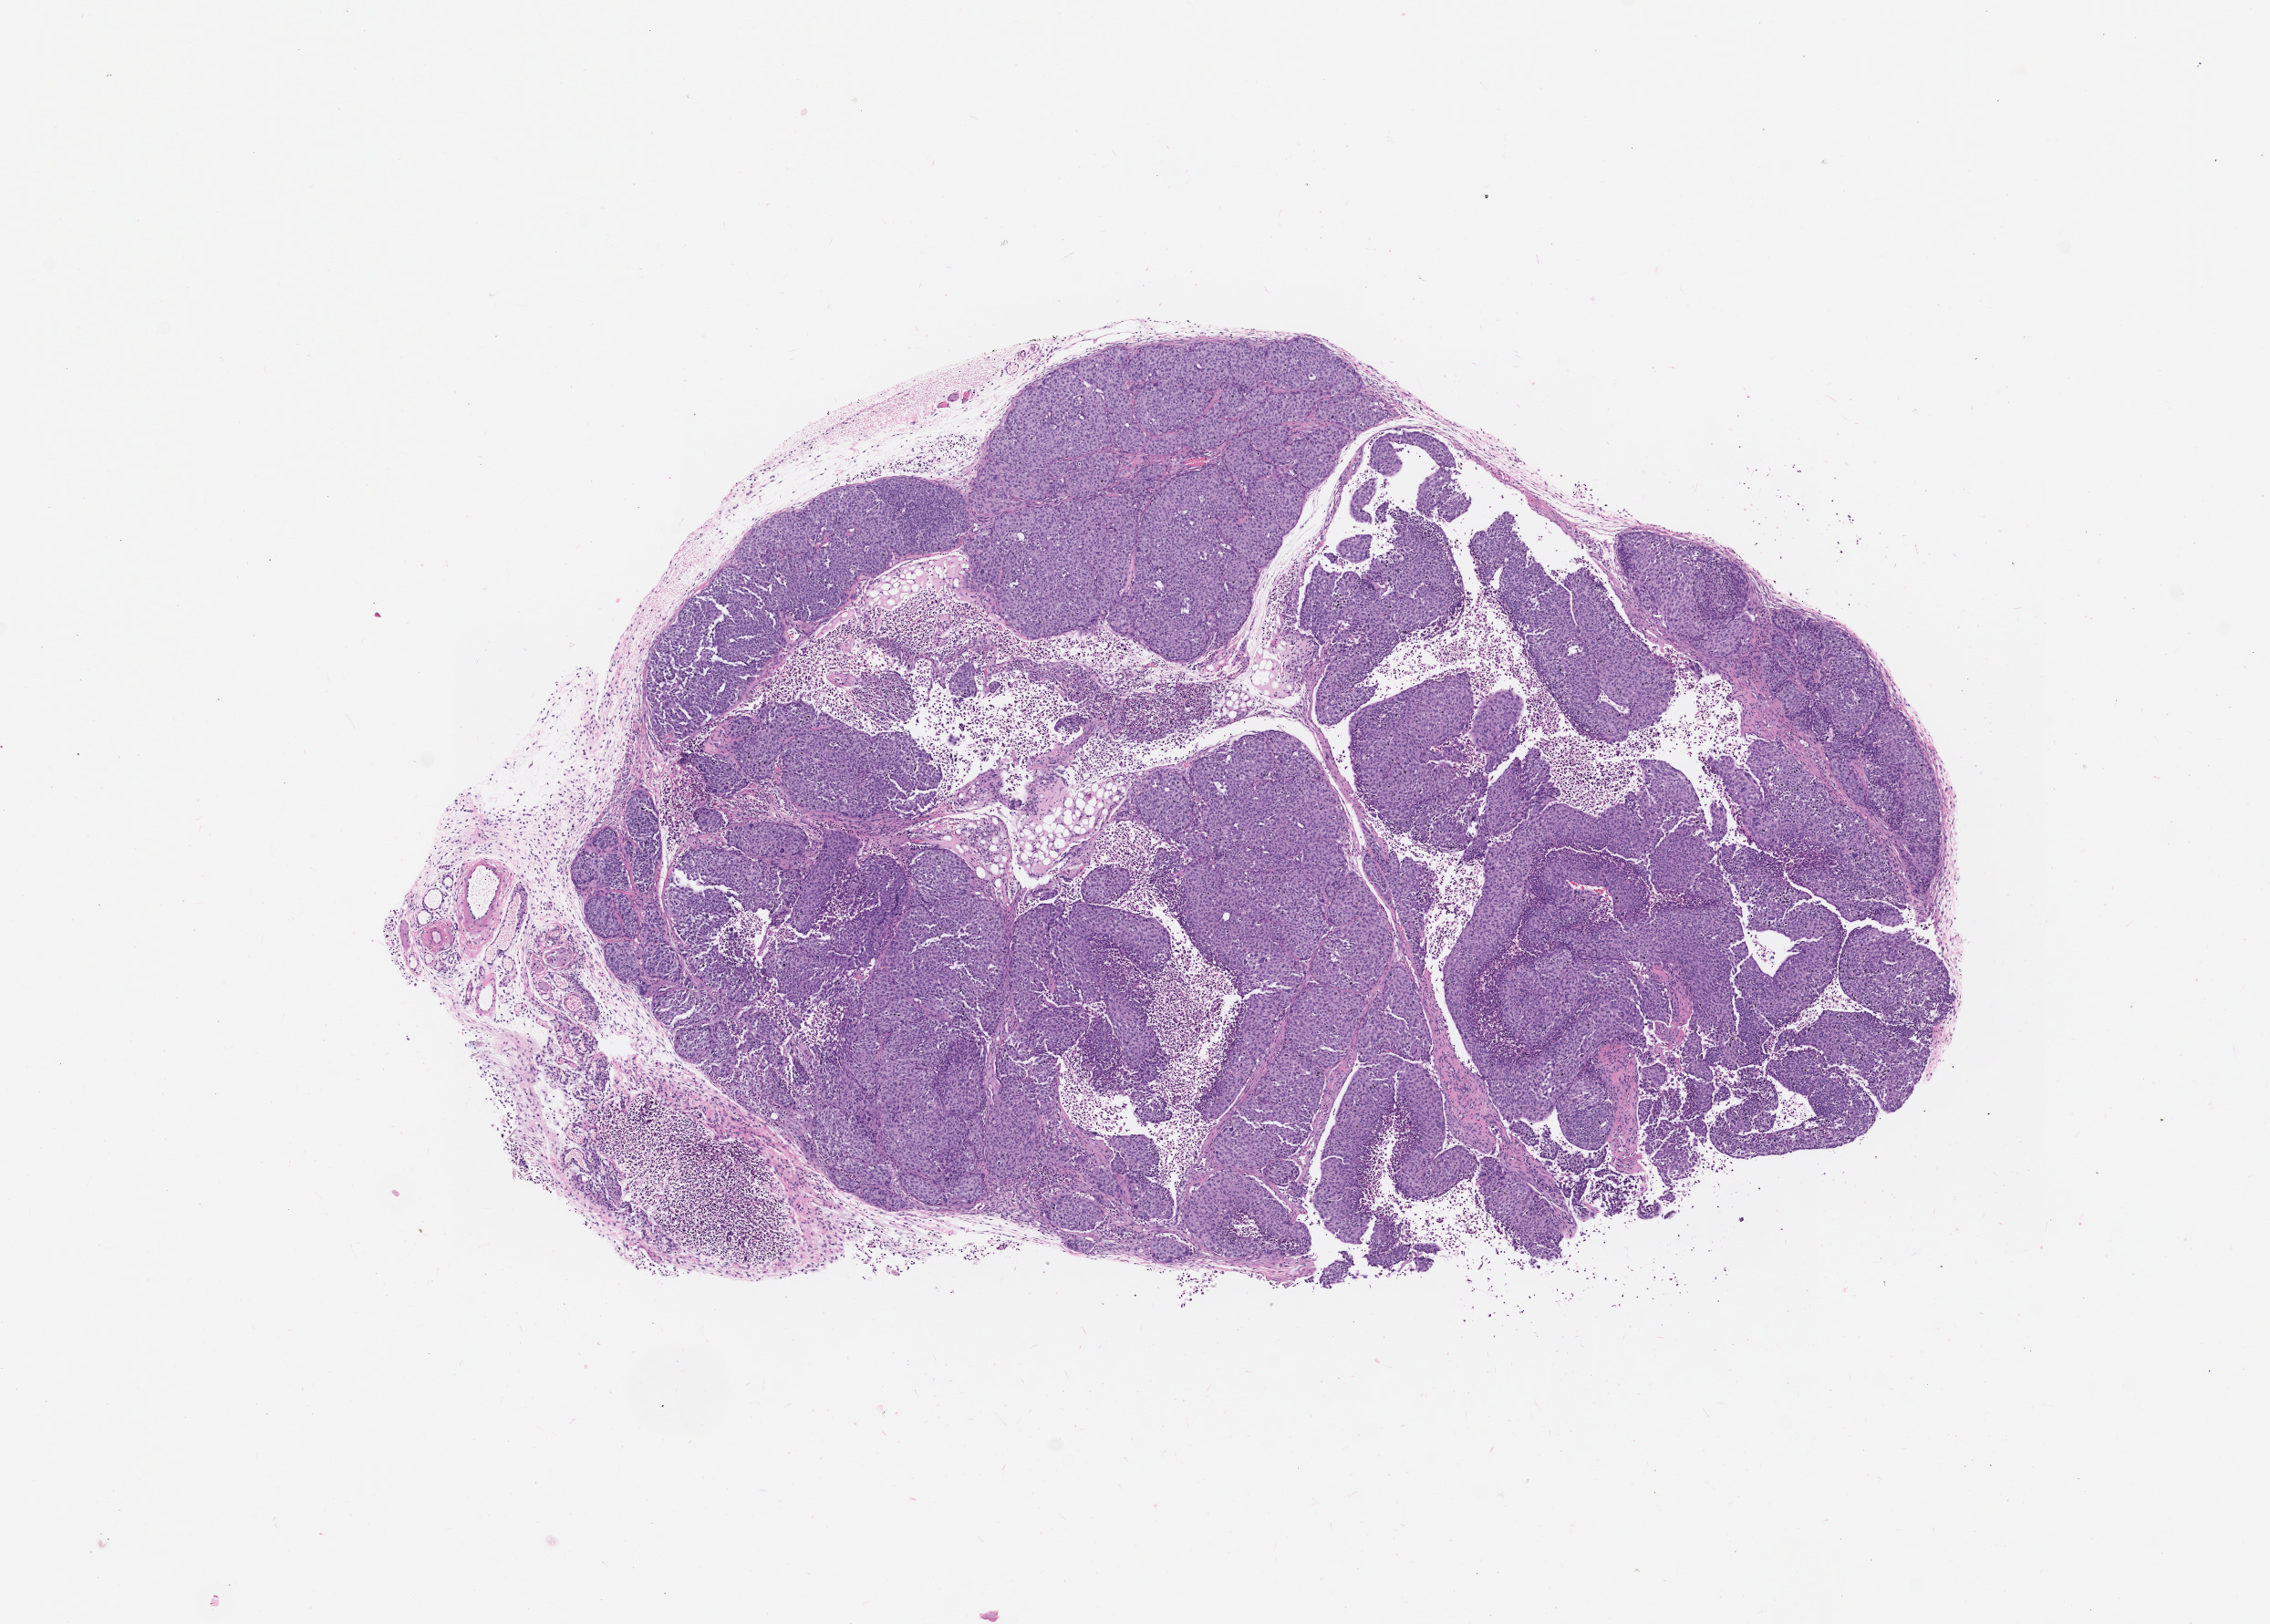
Whole-slide image, hematoxylin and eosin (H&E): patient-derived xenograft (human tumor grown in a mouse), passage 1, shown as a low-resolution overview of the whole scanned area (about 10.0 x 7.1 mm), formalin-fixed, paraffin-embedded (FFPE) tissue, tumor site category: head and neck.
Originating patient diagnosis: Head and Neck Squamous Cell Carcinoma.